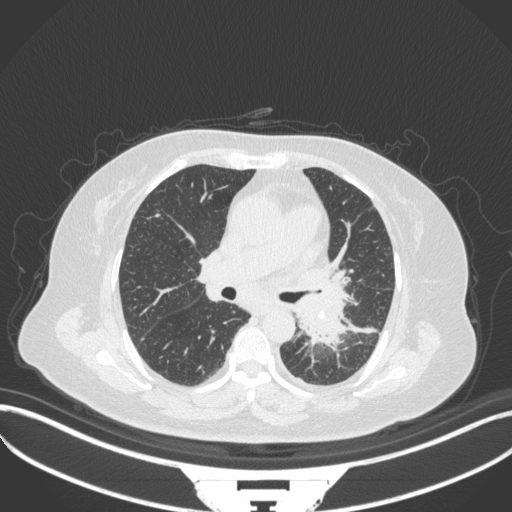
Chest CT, one axial slice. Position 199 of 328 along the scan axis. Lung window (W 1500 / L -600 HU). 1 mm slice thickness. 512 × 512 image matrix, field of view 400 × 400 mm. Female patient, age 69 years. From the clinical record (not read from this slice): clinical TNM (as recorded): T2b N3 M1.
Annotated regions visible in this slice (rectangle marked by the reading radiologist):
- lung tumour (recorded histology: adenocarcinoma): bounding box <288,288,352,350> (left, top, right, bottom; pixels)